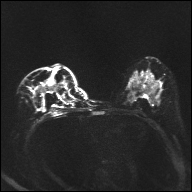
Breast MRI, one axial slice; slice 18 of 32 in the series (ordered by position); diffusion-weighted series; image 2 of 4 stored at this slice position (different b-values; order by instance number); 1.5 T; 4 mm slice thickness; 192 × 192 image matrix, field of view 360 × 360 mm. Female patient.
Structures marked on this image (expert manual segmentation):
- tumour on diffusion-weighted imaging: bounding box (x1, y1, x2, y2) in pixels: (42, 86, 59, 92)